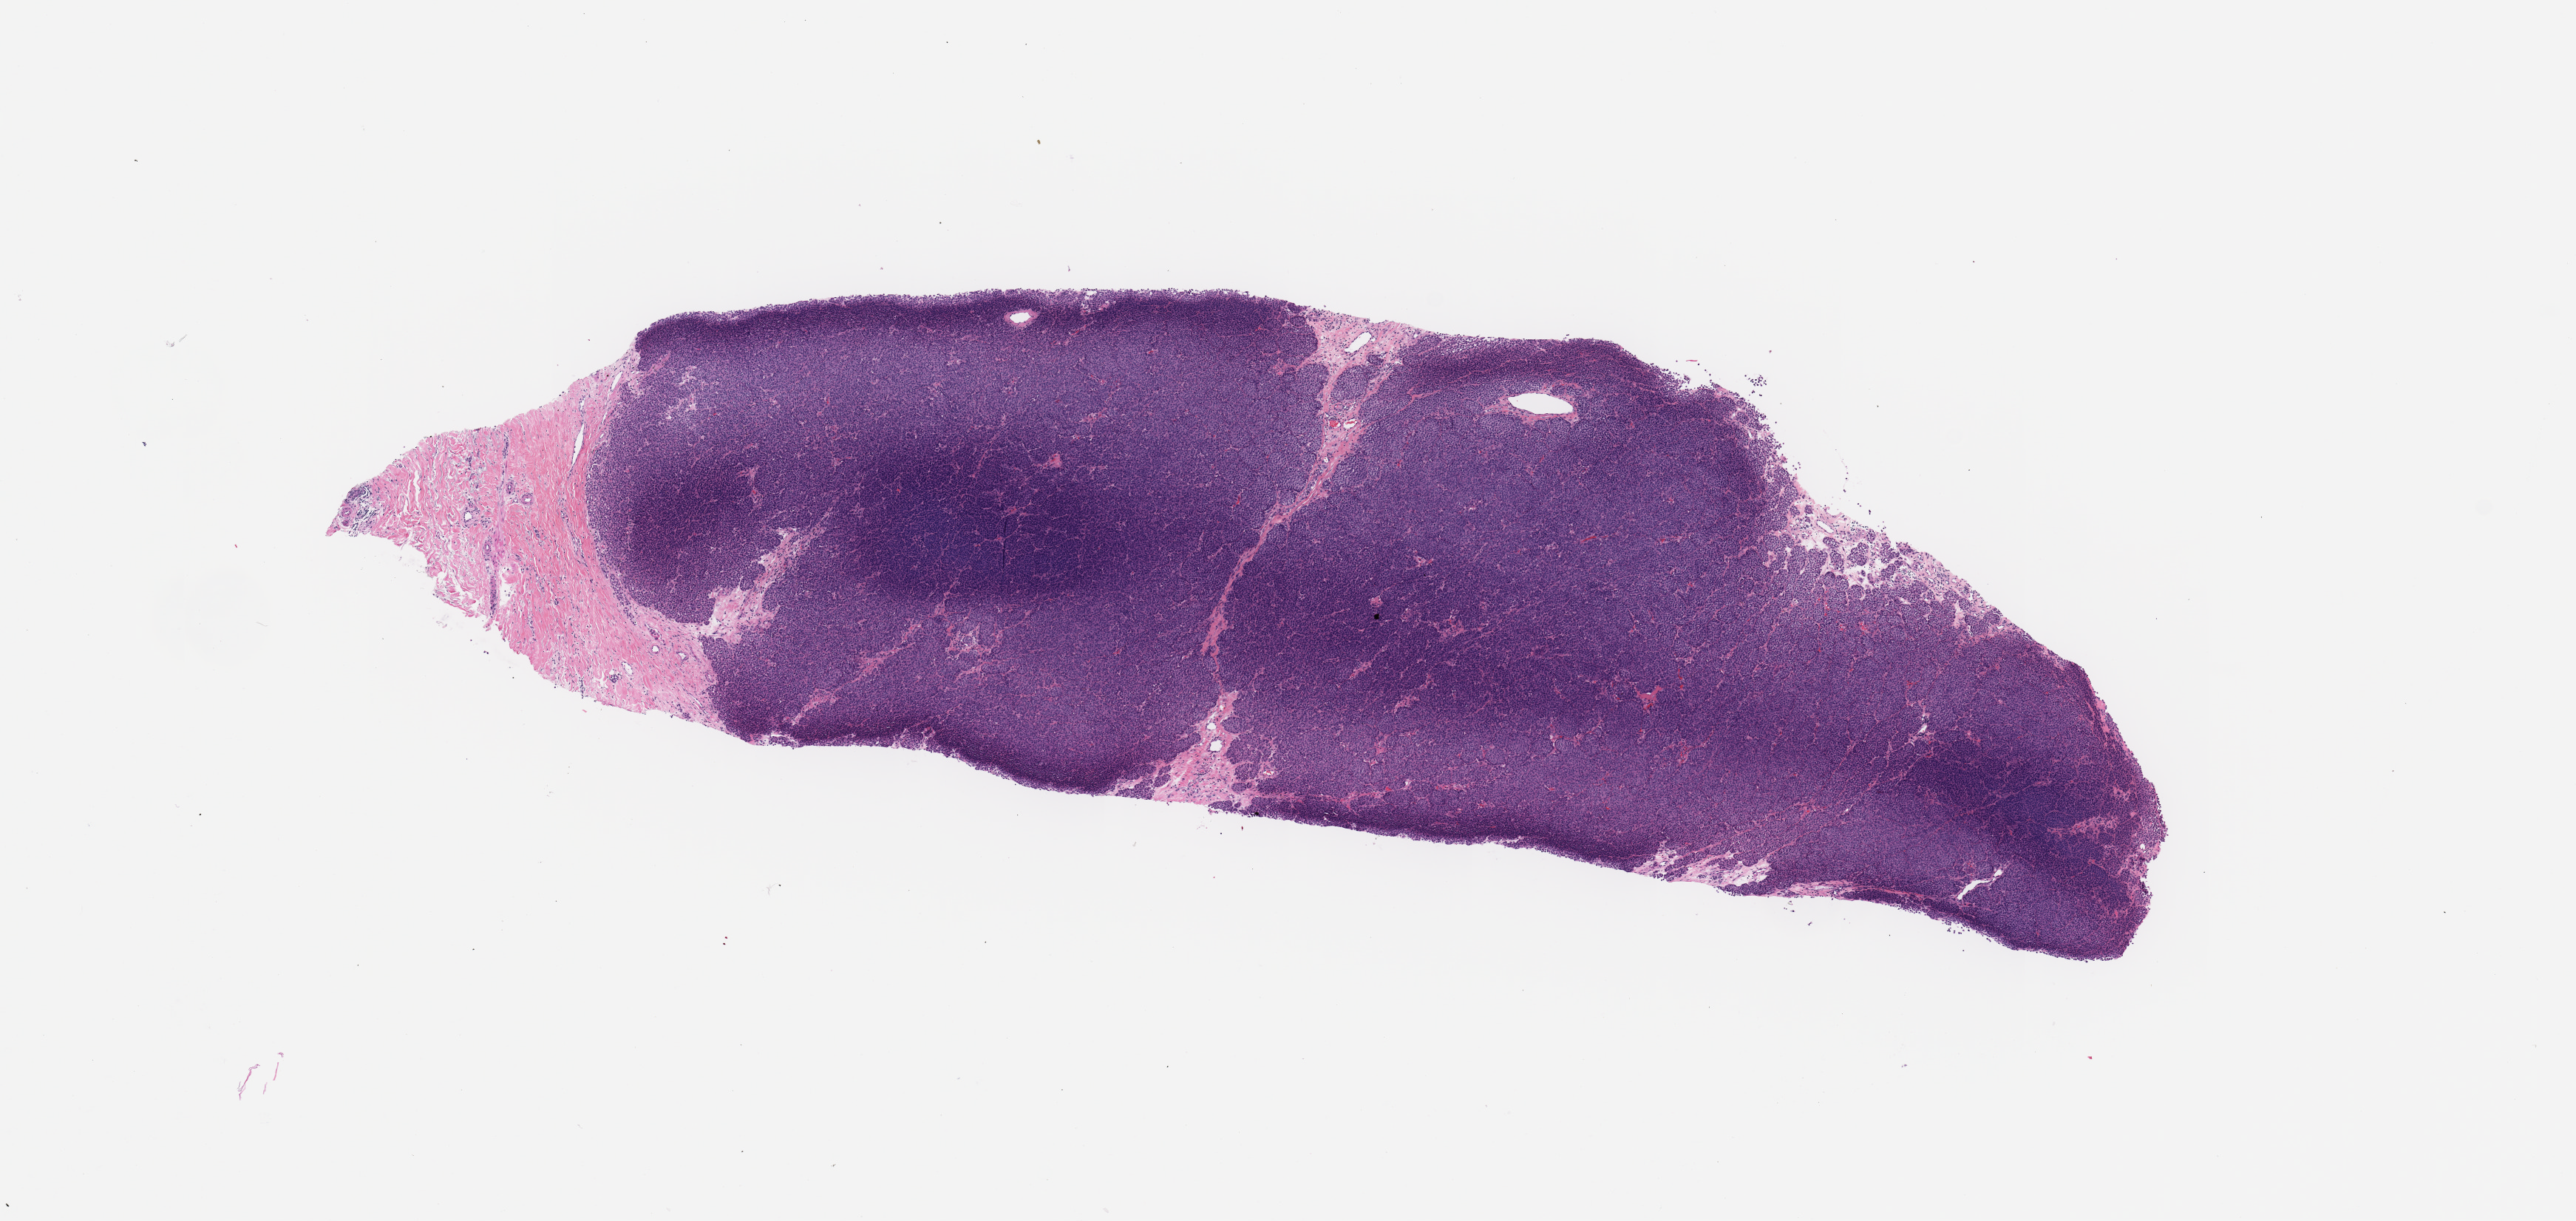
Digitized H&E tissue section (whole slide), whole scanned area (about 13.8 x 6.5 mm) shown as a low-resolution overview. Tumour tissue sample, sampled site: skin. Patient: male, age 71 years. Slide review estimates, as recorded: tumour nuclei 95%, necrosis 0%.
Primary tumour site (as recorded): extremities. AJCC pathologic stage: IIC. Histologic diagnosis: Malignant melanoma, NOS.